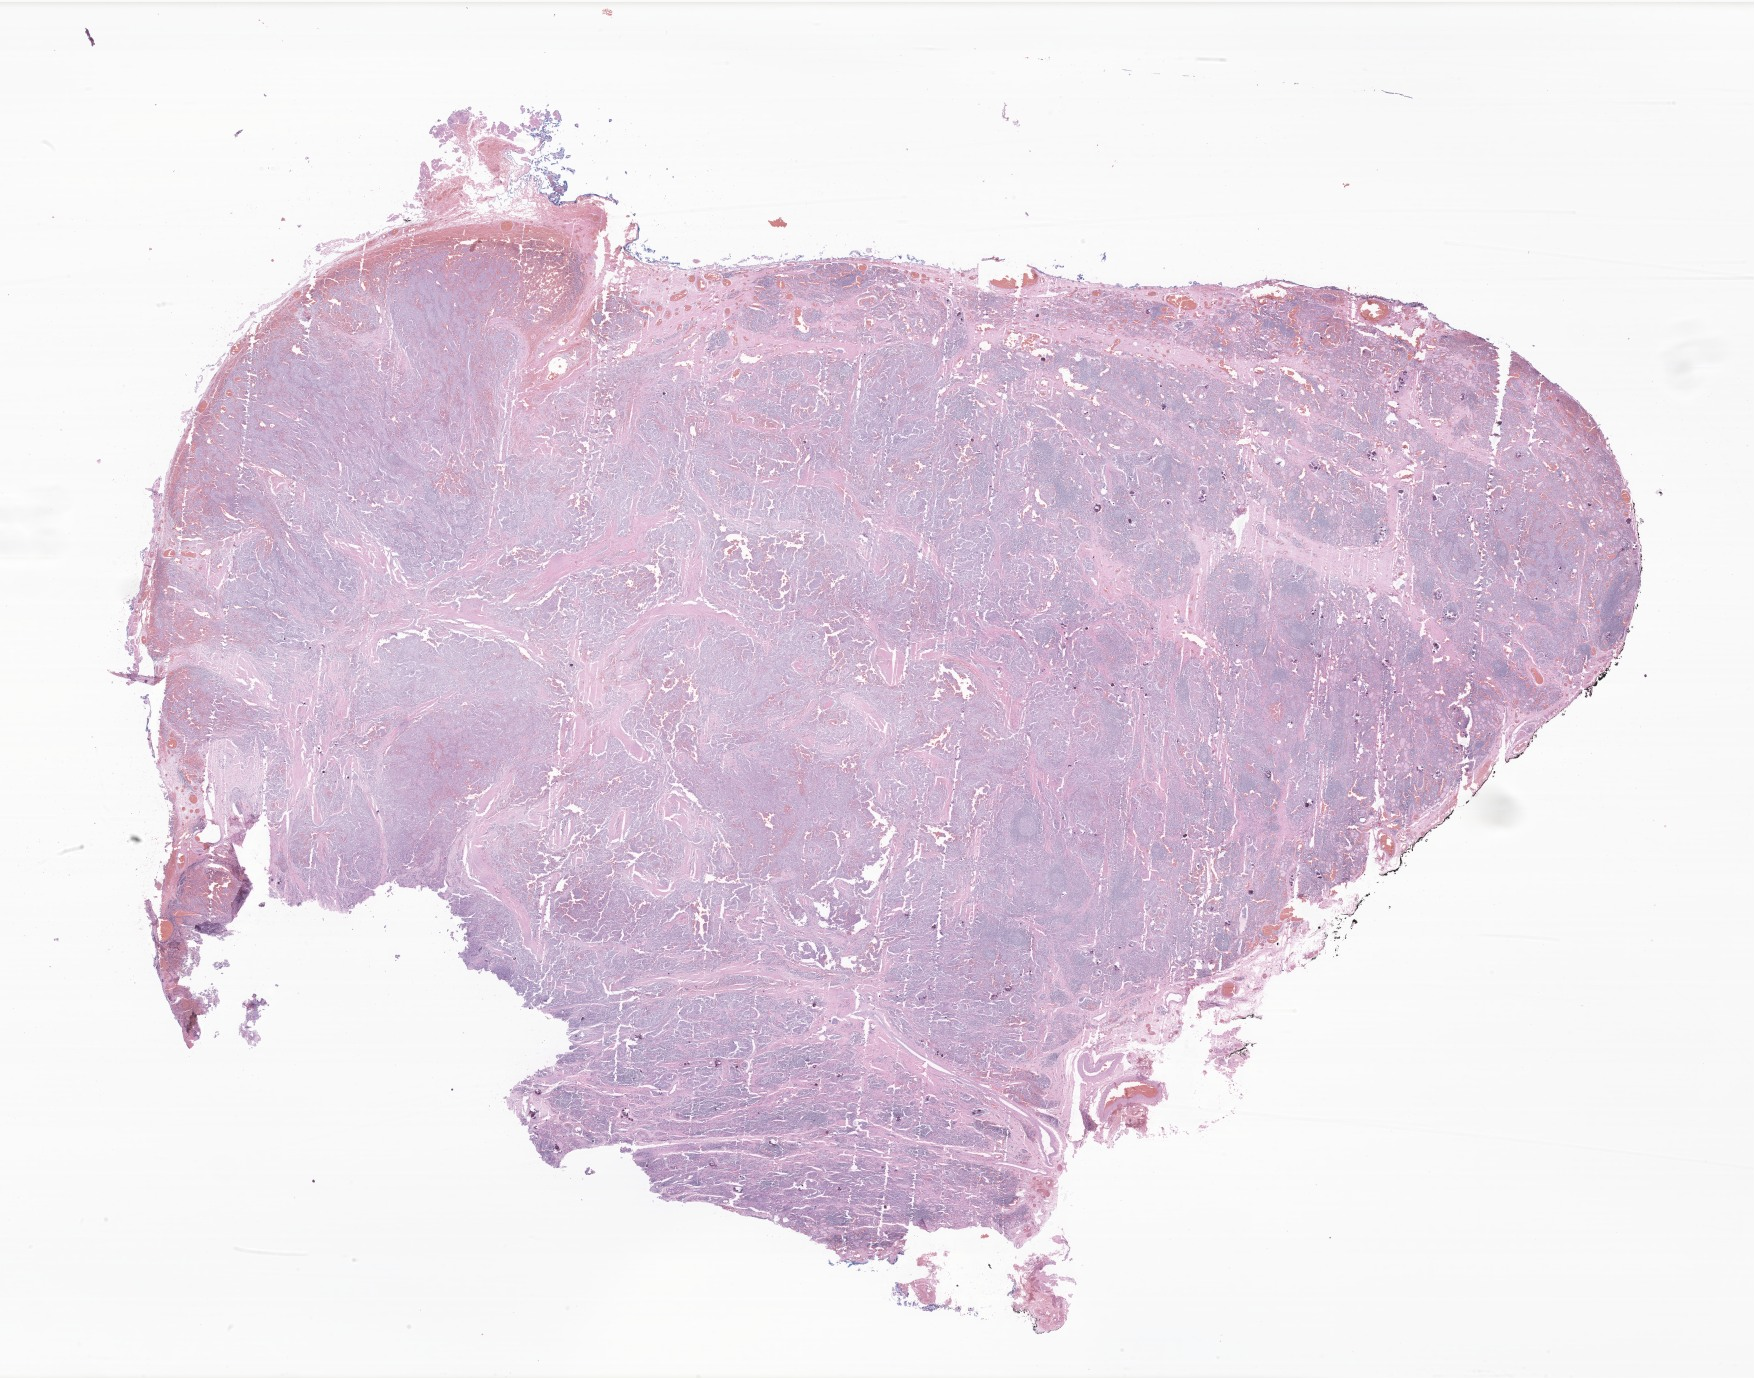
Hematoxylin and eosin (H&E) whole-slide image of tumor tissue from the thyroid — whole scanned area (about 29.6 x 23.2 mm) shown as a low-resolution overview, FFPE section. Patient female; age 165 months (13 years 9 months).
Diagnosis: Papillary carcinoma, NOS.